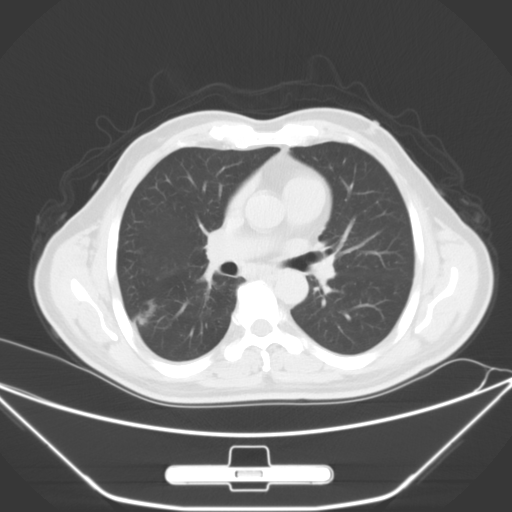
Chest CT, one axial slice; position 32 of 62 along the scan axis; 120 kVp; lung window (W 1500 / L -600 HU); 5 mm slice thickness; 512 × 512 image matrix. Patient: male, 71 years. From the clinical record (not read from this slice): clinical TNM (as recorded): T1c N0 M0.
Outlined on this slice (rectangle marked by the reading radiologist):
- lung tumour (recorded histology: adenocarcinoma): bounding box <130,298,165,327> (left, top, right, bottom; pixels)